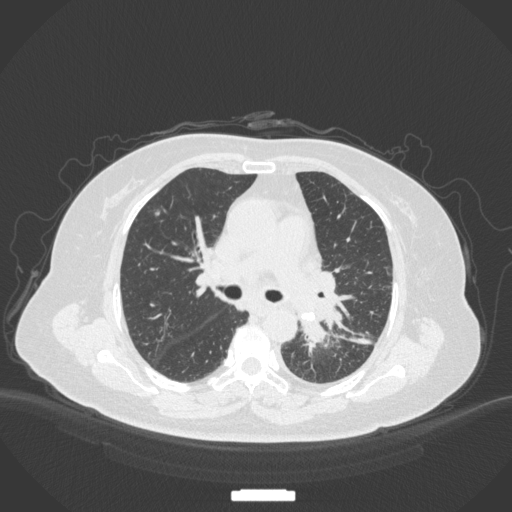
Chest CT, one axial slice. 120 kVp. Lung window (W 1500 / L -600 HU). 1 mm slice thickness. 512 × 512 image matrix, field of view 400 × 400 mm. Patient: female, 69 years. From the clinical record (not read from this slice): clinical TNM (as recorded): T2b N3 M1.
Outlined on this slice (rectangle marked by the reading radiologist):
- lung tumour (recorded histology: adenocarcinoma): bounding box (x1, y1, x2, y2) in pixels: (298, 310, 334, 355)